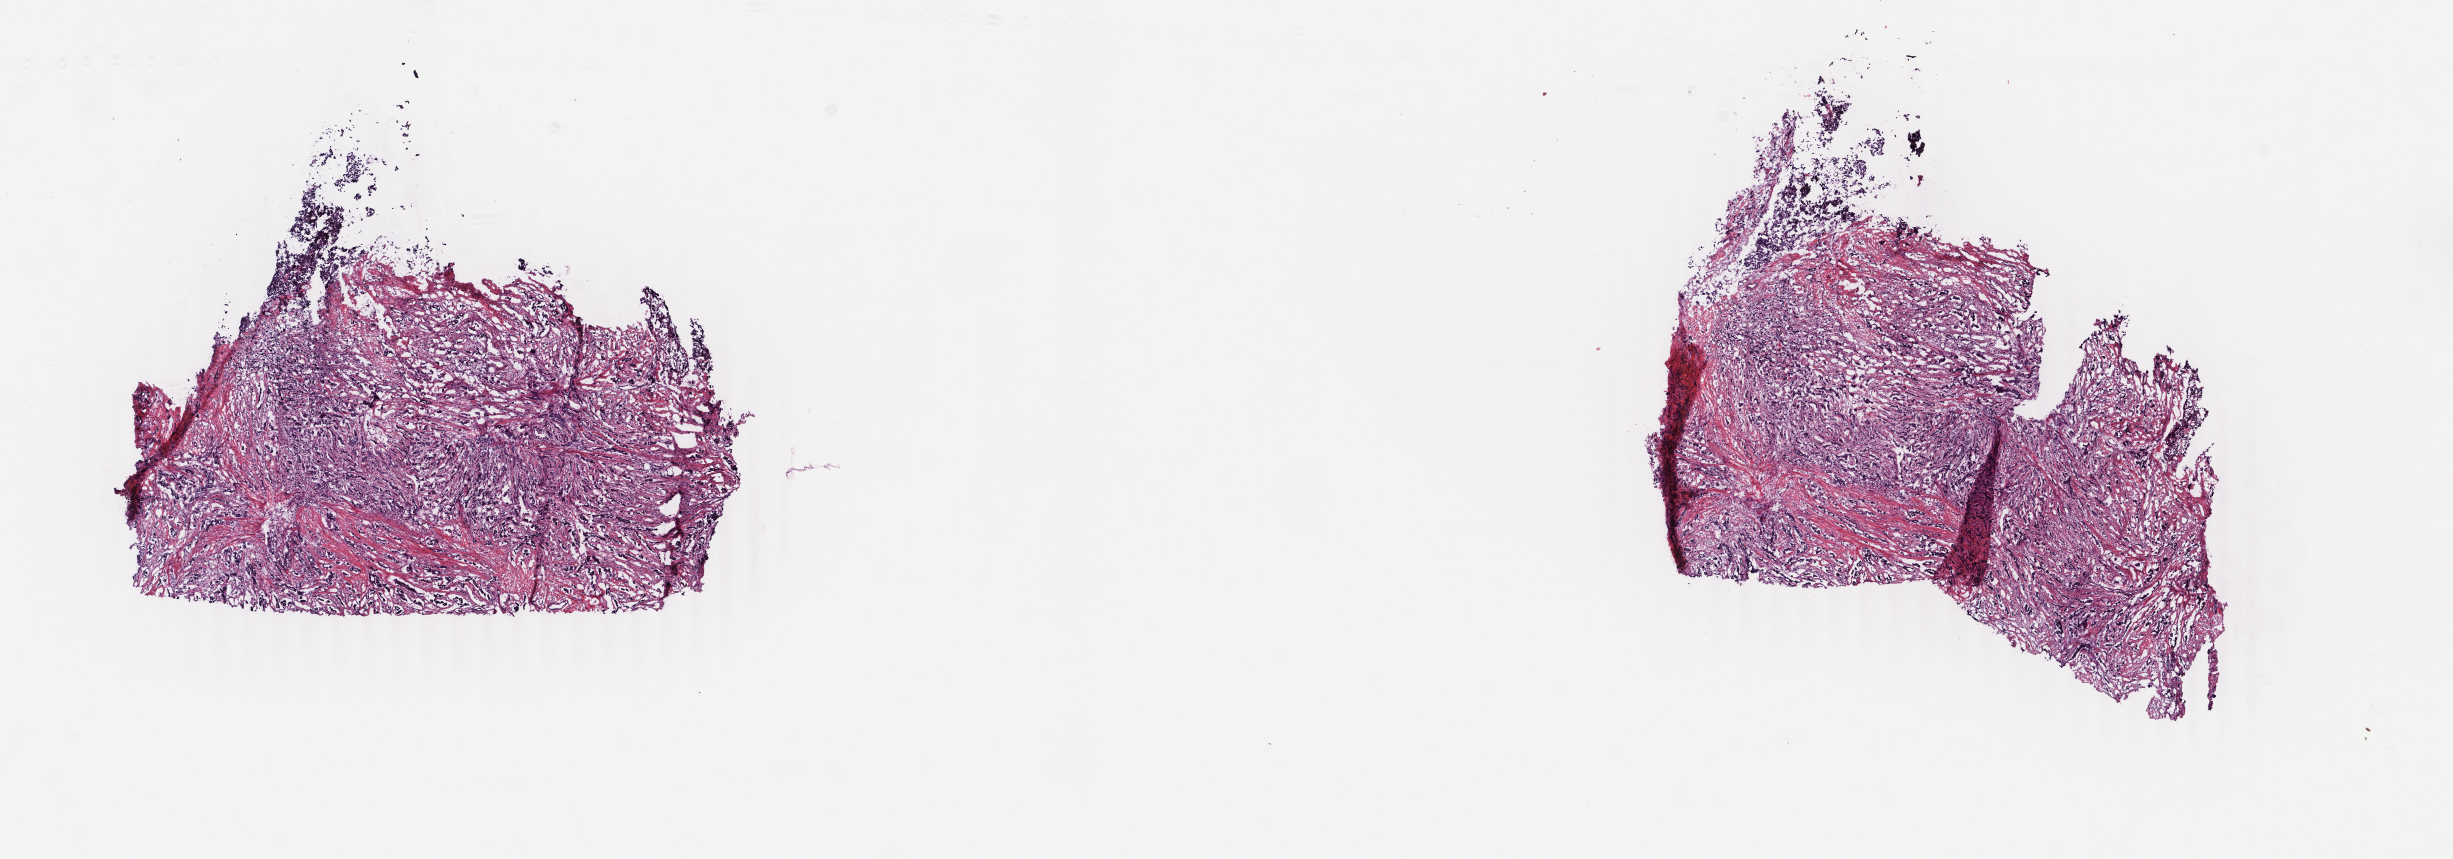
H&E-stained whole-slide image, low-resolution overview of the scanned area, about 19.5 x 6.8 mm (slide scanned at 40x). Frozen section from the bottom of the tissue portion. Primary tumour sample from the breast. Female, age 64 years at initial diagnosis. Slide review estimates, as recorded: tumour cells 85%, tumour nuclei 85%, normal cells 0%, stromal cells 15%, necrosis 0%. Infiltration values recorded for this section: lymphocyte infiltration 1%, monocyte infiltration 0%, neutrophil infiltration 0%.
Pathologic diagnosis: Infiltrating duct carcinoma, NOS. Laterality: right. Lymph nodes positive (case pathology): 8 of 15 examined. TNM: T3 N3 M1. AJCC pathologic stage: IV (3rd edition).